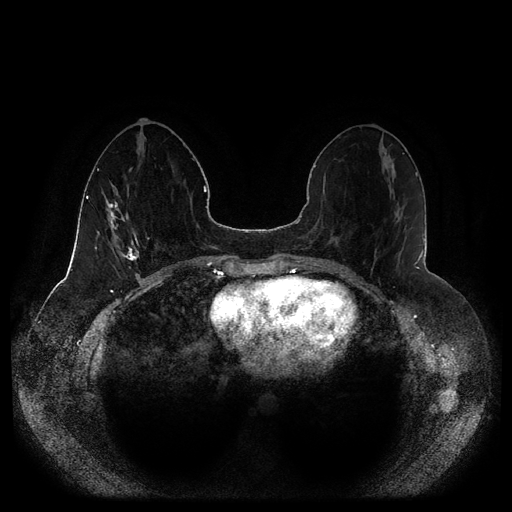
Breast MRI (dynamic contrast-enhanced, multi-phase), one axial slice; position 39 of 116 along the scan axis; dynamic contrast-enhanced series, time point 2 of 5 at this slice position (early post-contrast); 1.5 T; TE 2.5 ms, TR 5.2 ms; 512 × 512 image matrix, field of view 390 × 390 mm. Female patient, age 44 years.
Outlined on this slice (semi-automatic segmentation, software-assisted and operator-edited):
- breast lesion (labelled 'tumour' in the annotation; benign lesions carry a separate 'benign' label): bounding box (x1, y1, x2, y2) in pixels: (118, 241, 139, 265)
- breast lesion (labelled 'tumour' in the annotation; benign lesions carry a separate 'benign' label): (101, 191, 128, 244)